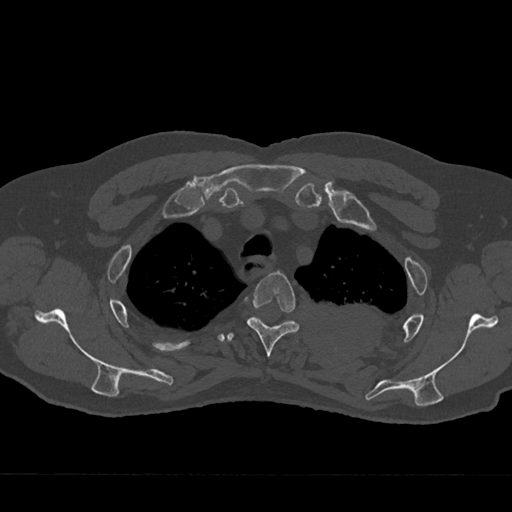
CT including the spine, one axial slice; position 563 of 797 along the scan axis; reconstruction kernel Br40s/3; bone window (W 1800 / L 400 HU); 0.5 mm slice thickness; 512 × 512 image matrix. Male patient, age 75 years. Case-level facts recorded for this patient, not image findings: primary cancer: renal; vertebrae with lytic lesions (as recorded): T4.
Structures marked on this image (semi-automatic segmentation, software-assisted and operator-edited):
- T3 vertebra: box from (x=246, y=271) to (x=300, y=357) px
- T4 vertebra: (x=227, y=317)–(x=287, y=341)